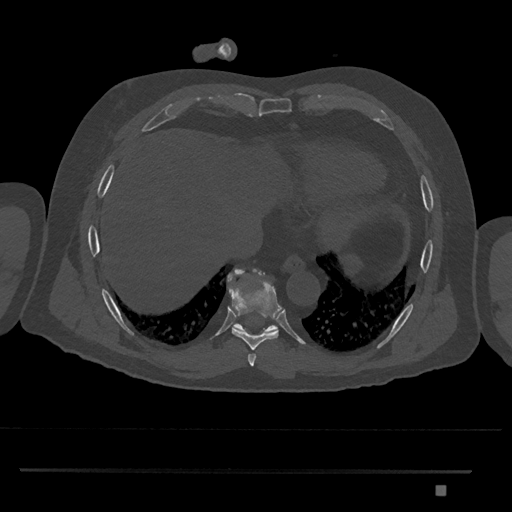
CT including the spine, one axial slice. Position 1094 of 1134 along the scan axis. Reconstruction kernel Br40s/3. 120 kVp. Bone window (W 1800 / L 400 HU). 512 × 512 image matrix. Male patient, age 65 years. Case-level facts recorded for this patient, not image findings: primary cancer: prostate.
Annotated regions visible in this slice (semi-automatically segmented with operator editing):
- T8 vertebra: bounding box [x1, y1, x2, y2] px = [230, 269, 283, 349]
- T9 vertebra: [227, 268, 278, 333]